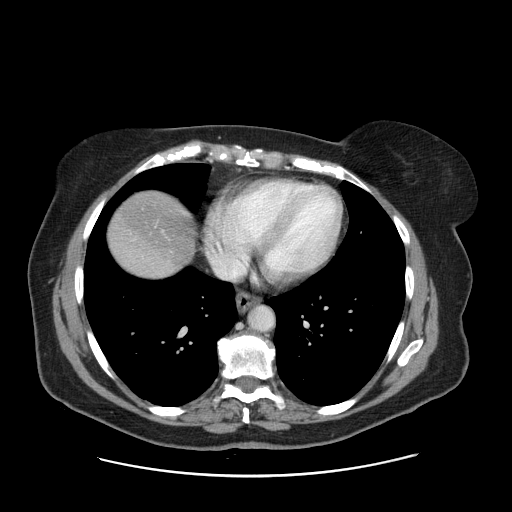
Contrast-enhanced abdominal CT, one axial slice. Intravenous contrast given. Soft-tissue window (W 400 / L 40 HU). 2.5 mm slice thickness. 512 × 512 image matrix, field of view 398 × 398 mm. Female patient, age 62 years. Case-level facts recorded for this patient, not image findings: diagnosis: colorectal cancer liver metastases, imaged before liver resection; multiple liver metastases: no; largest metastasis: 2.5 cm; chemotherapy before resection: yes.
Structures marked on this image (expert manual segmentation):
- liver: bounding box [x1, y1, x2, y2] px = [109, 192, 196, 276]
- planned liver remnant (the part of the liver to remain after resection): [109, 192, 195, 268]